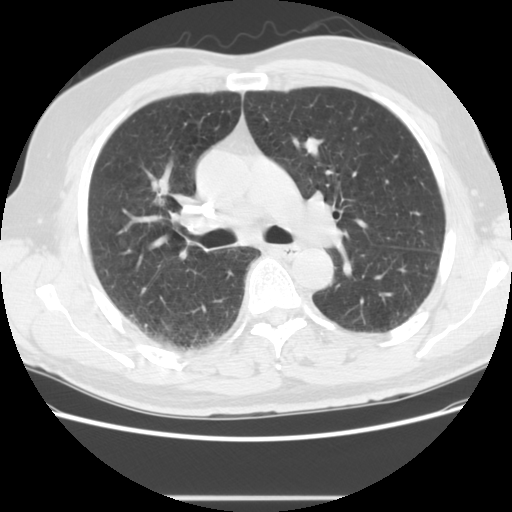
Axial slice from a low-dose chest CT screening exam; second screening round (one year after baseline); lung window (W 1500 / L -600 HU); standard (soft-tissue) reconstruction kernel (STANDARD); 120 kVp; slice 56 of 139 in the series; 512 × 512 image matrix, field of view 360 × 360 mm. Male participant, aged 59 years at enrolment. Current smoker at enrolment.
Expert-annotated lung lesion, box from (x=136, y=171) to (x=178, y=216) px. Reader record for this screening exam (exam-level; its link to the box is not recorded): non-calcified nodule or mass ≥4 mm, right upper lobe, 20 × 13 mm, spiculated (stellate) margins, soft tissue attenuation, pre-existing on the prior screen: yes; interval growth: yes. Participant outcome: lung cancer diagnosed 267 days after this screen — large cell carcinoma, NOS, right upper lobe, poorly differentiated (G3), stage IIIA (AJCC 6th edition), 34 mm at pathology.